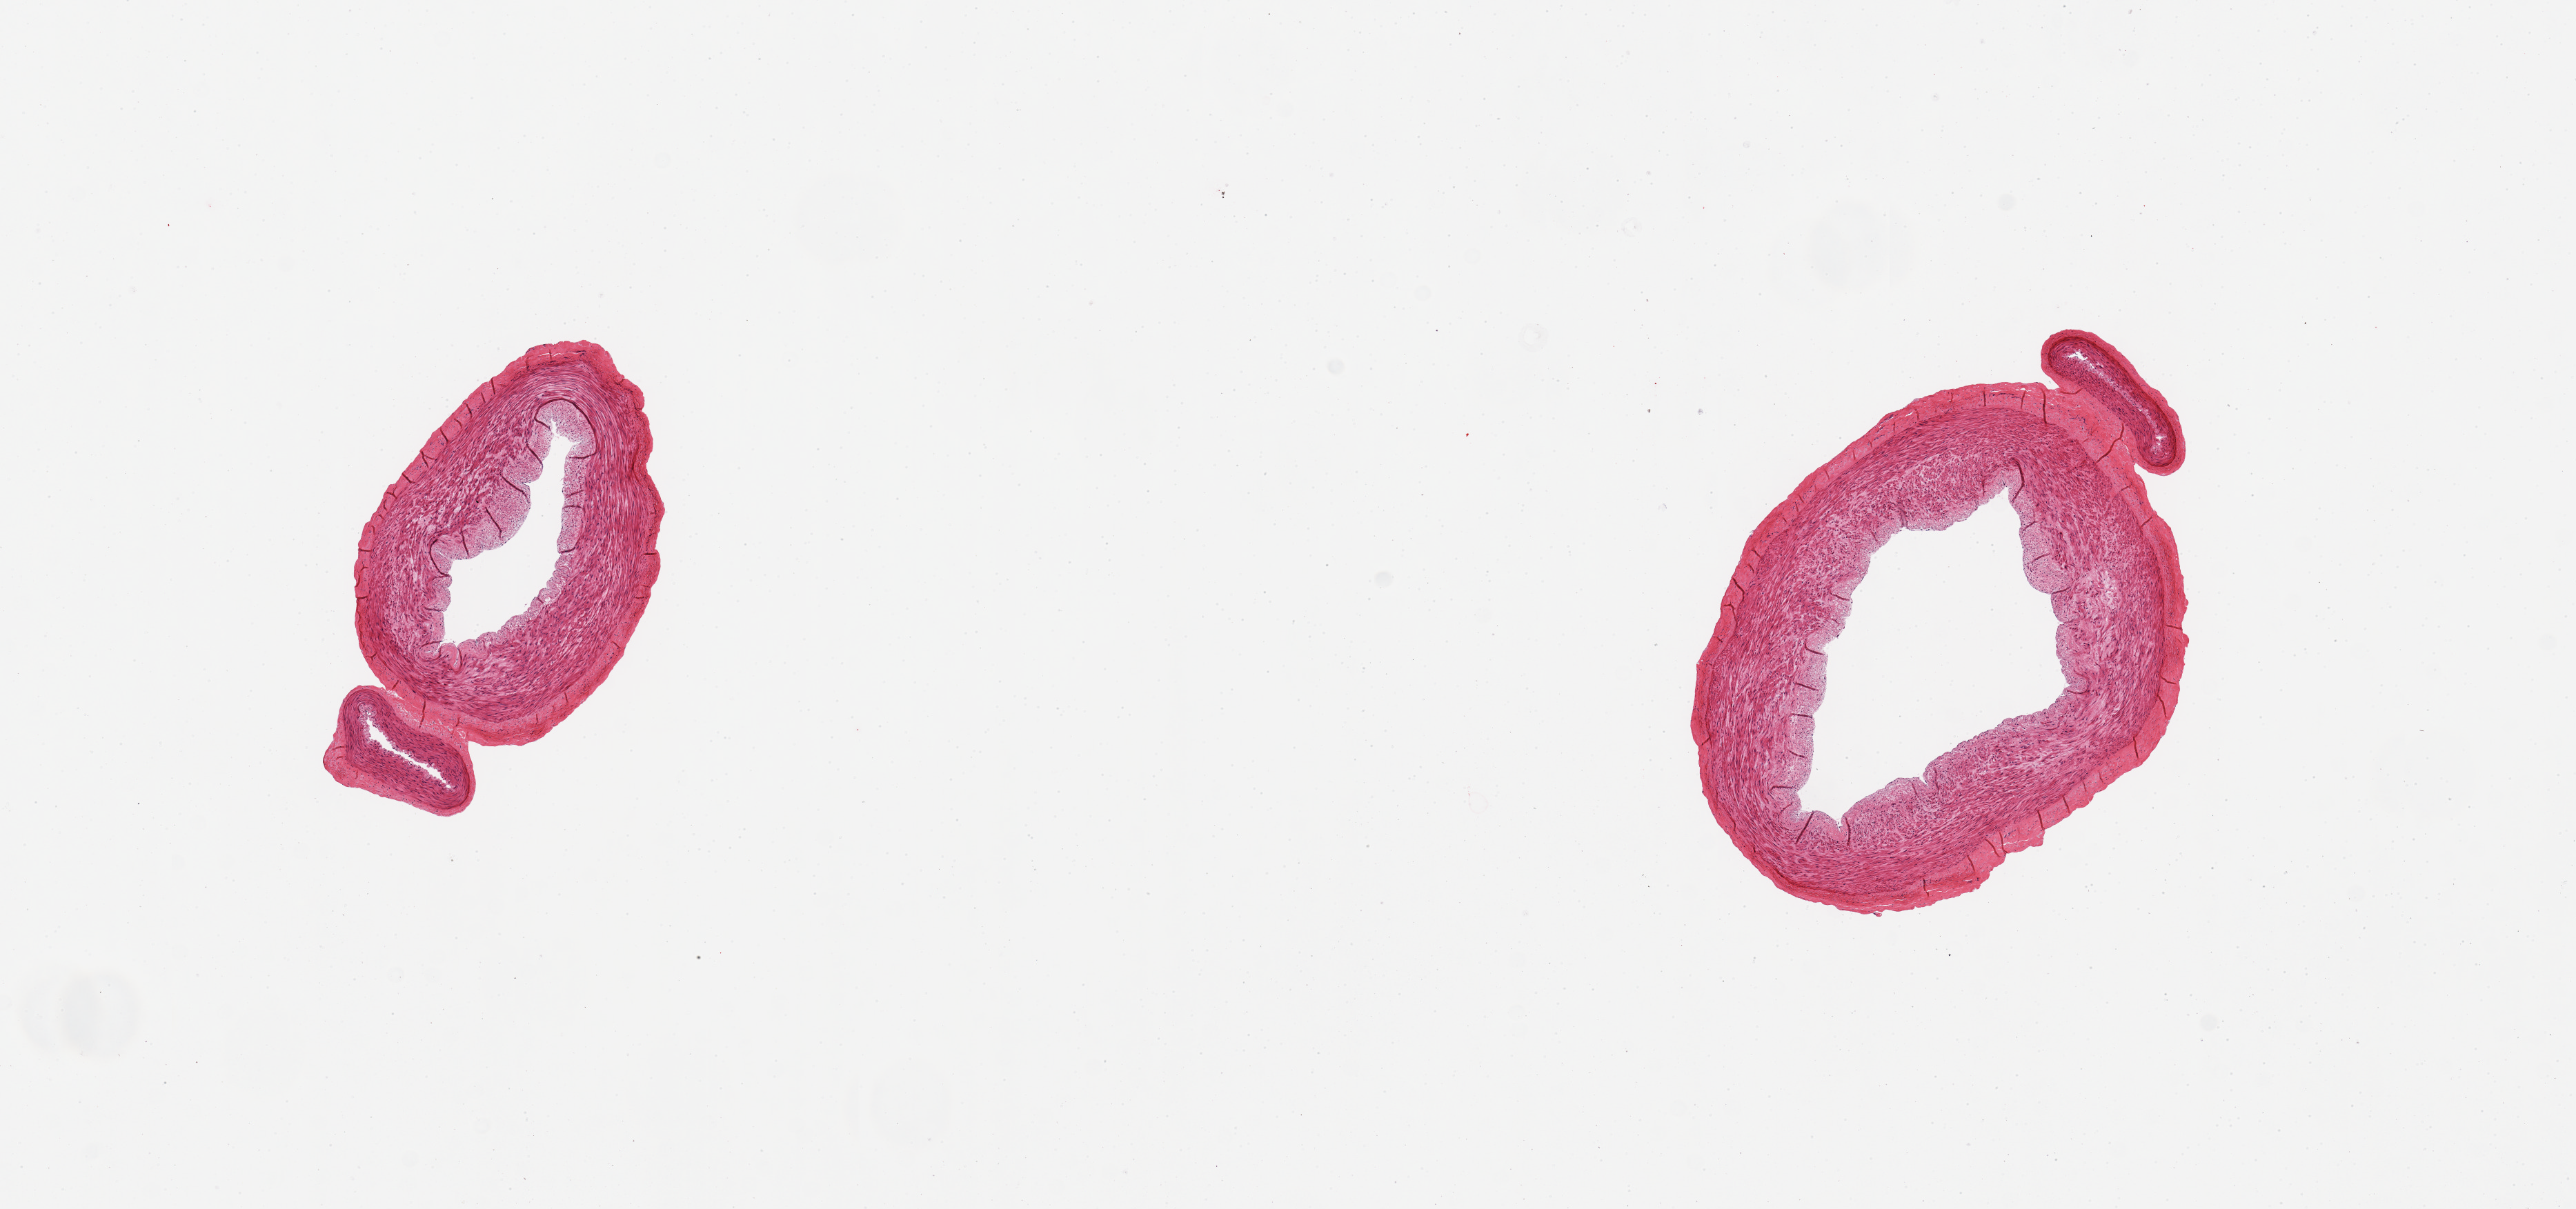
Digitized haematoxylin and eosin-stained section, low-resolution overview of the scanned area, about 14.8 x 6.9 mm (from a 20x scan). PAXgene-fixed paraffin-embedded (PFPE) section. Section of tibial artery (target tissue). Tissue donor sample. Male donor.
- reviewer comment on this tissue sample: 2 pieces, clean specimens; no adherent fat